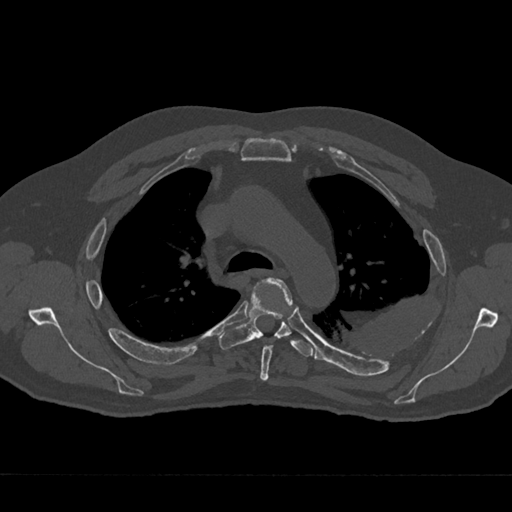
CT including the spine, one axial slice; slice 494 of 797 in the series (ordered by position); reconstruction kernel Br40s/3; 120 kVp; bone window (W 1800 / L 400 HU); 512 × 512 image matrix, field of view 377 × 377 mm. Male patient, age 75 years. From the clinical record (not read from this slice): primary cancer: renal.
Structures marked on this image (semi-automatically segmented with operator editing):
- T4 vertebra: bounding box (x1, y1, x2, y2) in pixels: (259, 278, 293, 381)
- T5 vertebra: (219, 292, 314, 357)